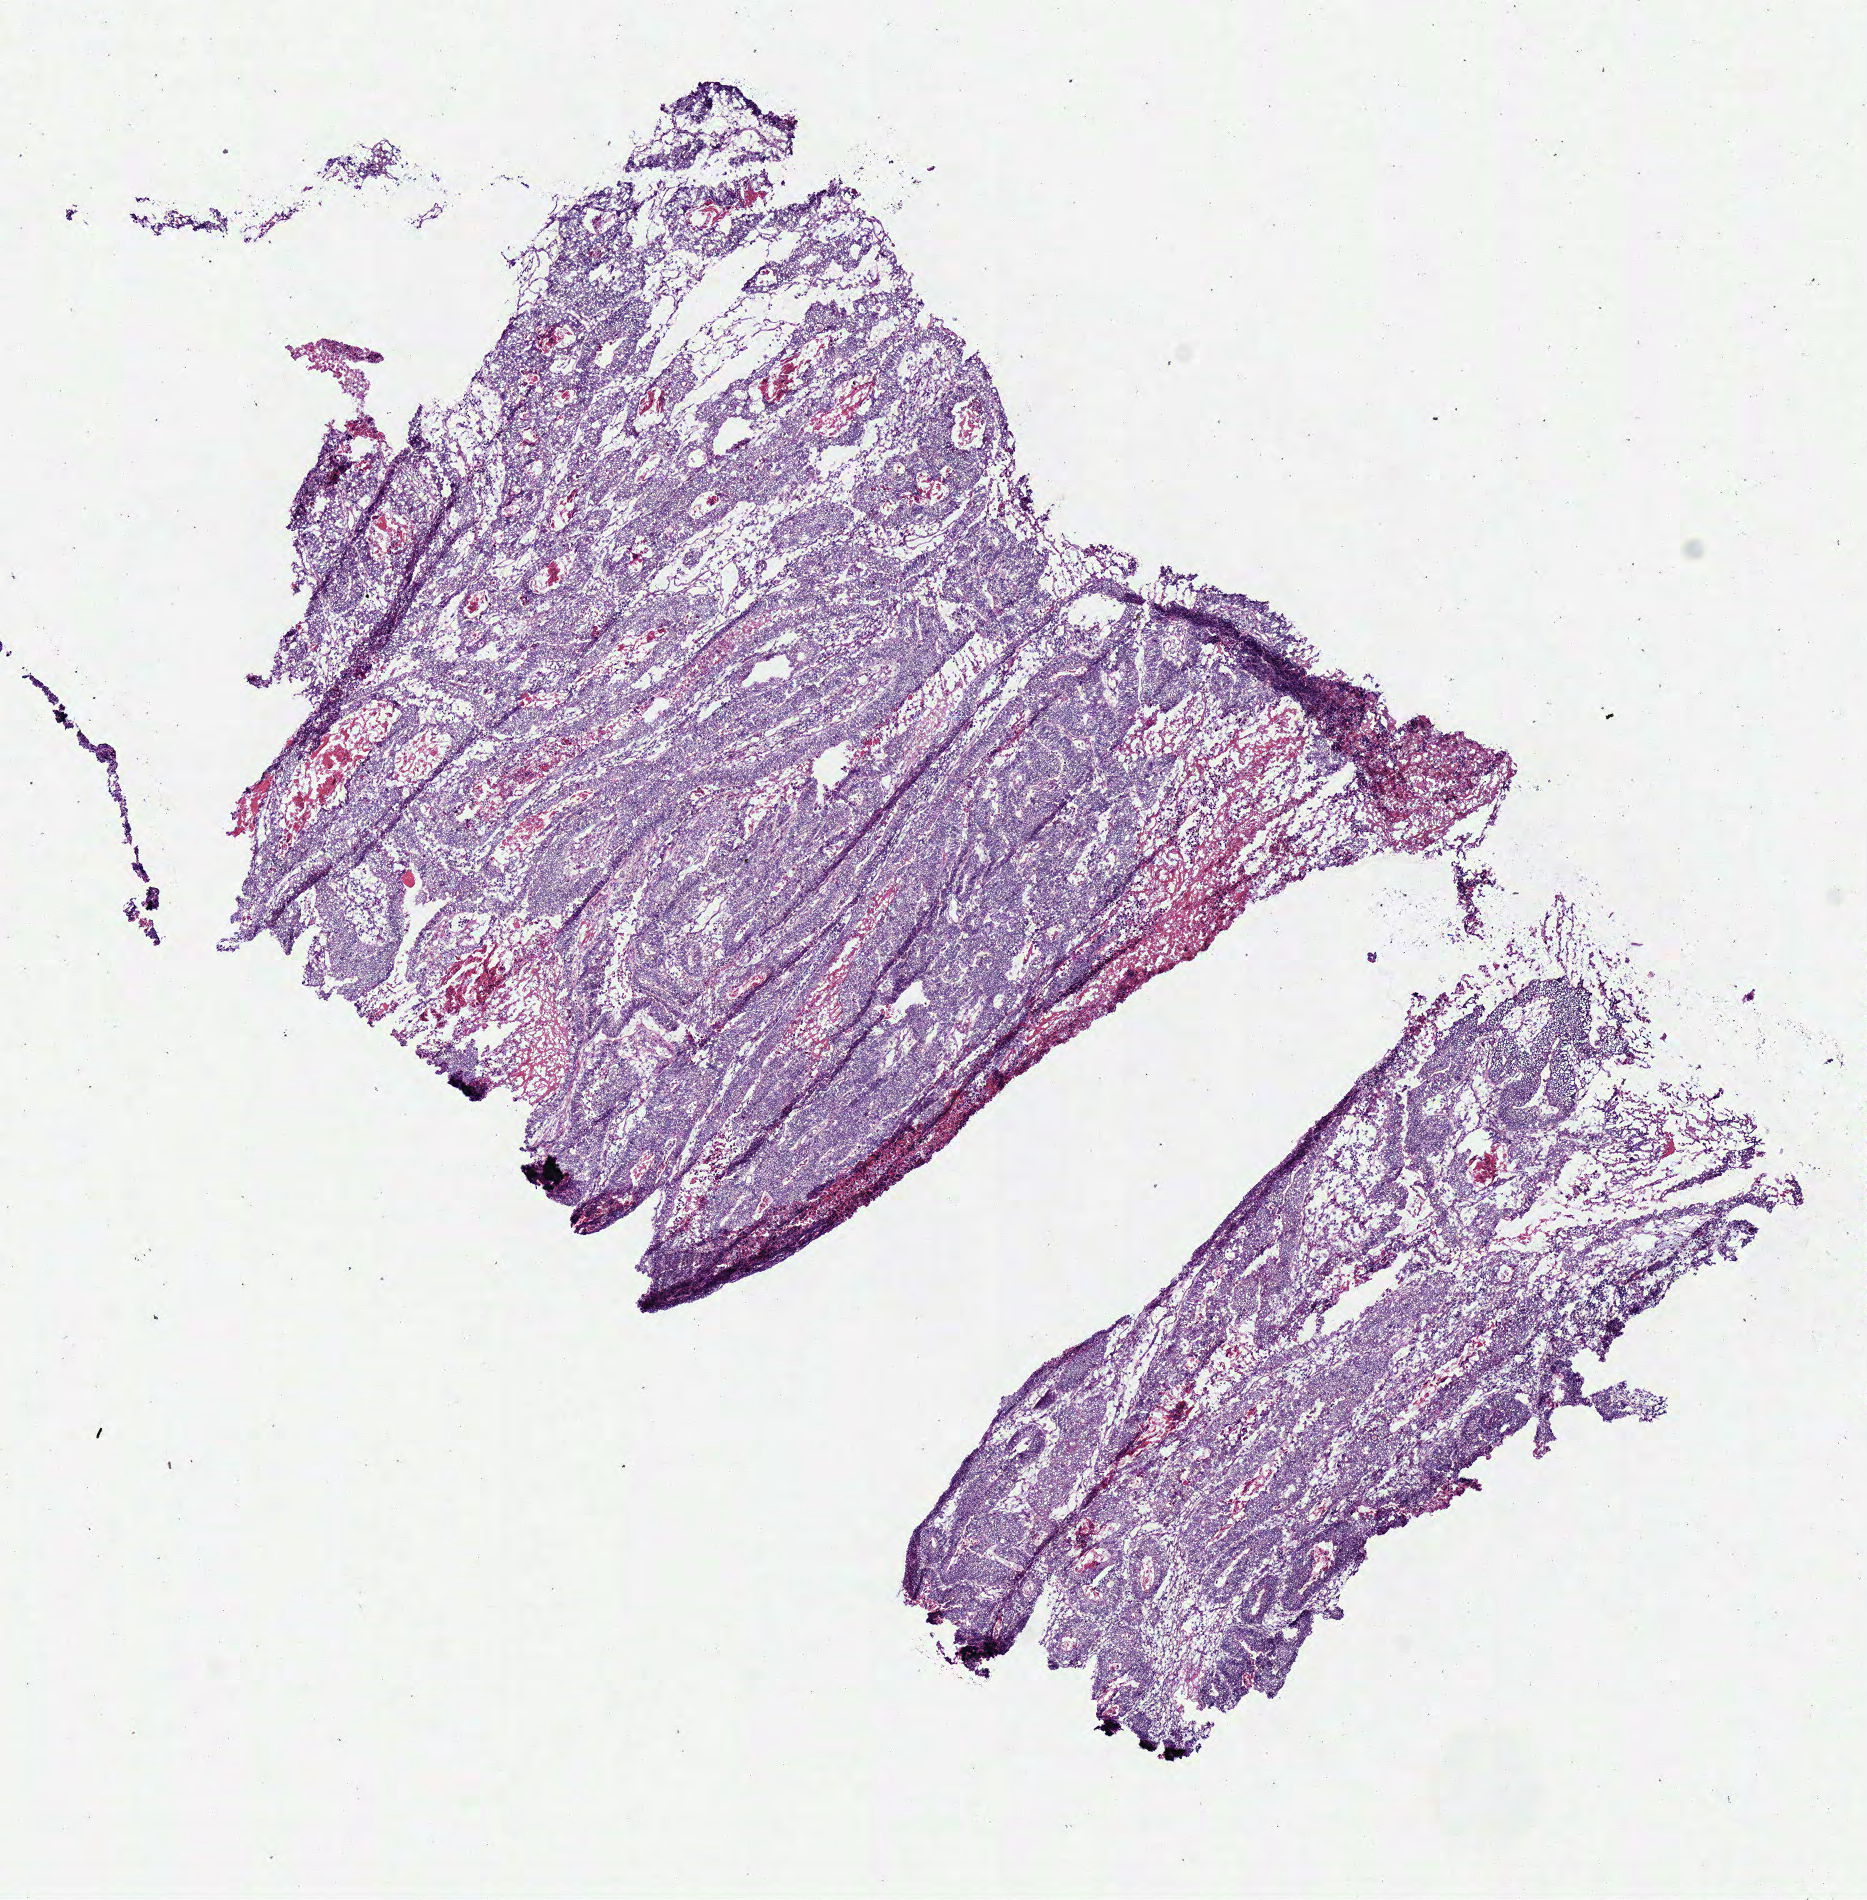
H&E whole-slide image, whole scanned area (about 7.3 x 7.5 mm, acquisition: 40x scan) shown as a low-resolution overview; frozen section; primary tumour sample from the colon. Female patient; age at initial diagnosis 68 years. Pathologist review of this section (percent, as recorded): tumour cells 90%, tumour nuclei 90%, normal cells 0%, stromal cells 0%, necrosis 10%. Inflammatory infiltration, as recorded: lymphocyte infiltration 2%, monocyte infiltration 2%, neutrophil infiltration 2%.
Diagnosis: Adenocarcinoma, NOS (transverse colon). Lymph nodes positive (case pathology): 0 of 8 examined.